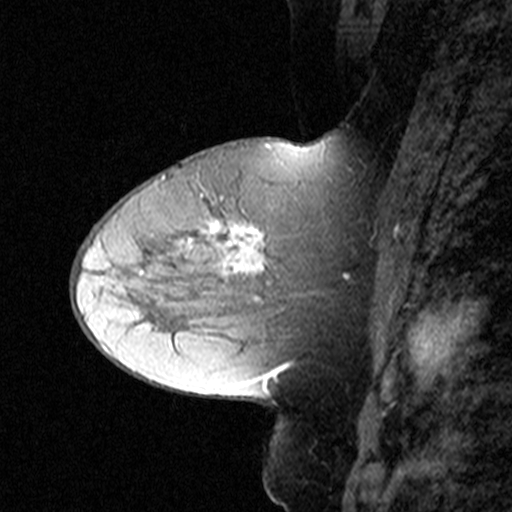
Breast MRI (dynamic contrast-enhanced), one sagittal slice. Position 21 of 44 along the scan axis. Dynamic contrast-enhanced study with each time point stored as its own series, time point 2 of 3 at this slice position (early post-contrast, ordered by acquisition time). 1.5 T. TE 4.5 ms, TR 11 ms. 3 mm slice thickness. 512 × 512 image matrix, field of view 200 × 200 mm. Female patient, age 50 years. Case-level facts recorded for this patient, not image findings: setting: breast cancer imaged before/during neoadjuvant chemotherapy; receptor status: HR-positive, HER2-negative.
Outlined on this slice (semi-automatically segmented with operator editing):
- analysis volume of interest (the breast-tissue region the enhancement analysis was run in; not a lesion): bounding box <180,198,349,311> (left, top, right, bottom; pixels)
- tumour enhancement mask (voxels above the 90 % enhancement threshold inside the analysis volume of interest): <184,219,349,301>